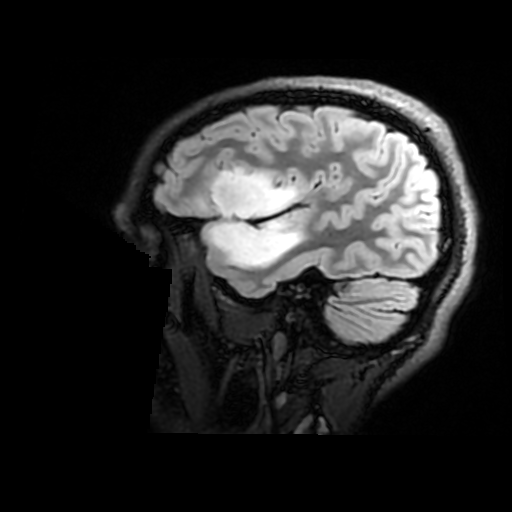
Brain MRI from a brain-tumour surgery series, one sagittal slice; slice 133 of 176 in the series (ordered by position); T2 FLAIR; 1 mm slice thickness; 512 × 512 image matrix, field of view 240 × 240 mm. From the clinical record (not read from this slice): histopathology: Astrocytoma; WHO grade: 2; IDH mutation: yes; tumour location: Right Insular.
Structures marked on this image (outlined manually by an expert reader):
- tumour: bounding box (x1, y1, x2, y2) in pixels: (211, 168, 304, 269)